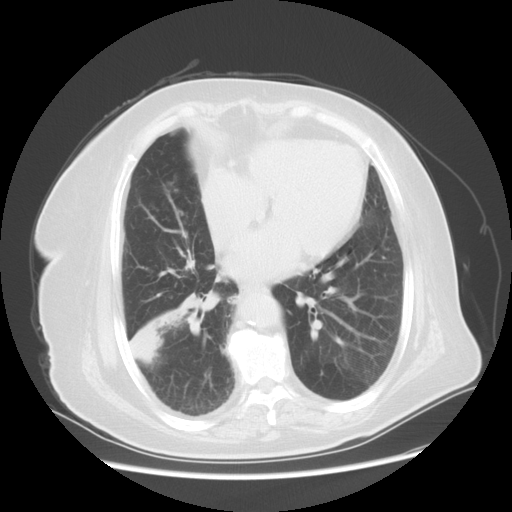
Chest CT, one axial slice; slice 23 of 56 in the series (ordered by position); reconstruction kernel STANDARD; lung window (W 1500 / L -600 HU); 5 mm slice thickness; 512 × 512 image matrix. Female patient, age 73 years. From the clinical record (not read from this slice): clinical TNM (as recorded): T3 N0 M0.
Outlined on this slice (rectangle marked by the reading radiologist):
- lung tumour (recorded histology: adenocarcinoma): box from (x=122, y=304) to (x=183, y=372) px